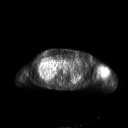
FDG PET of an extremity soft-tissue mass (from a PET/CT study), one axial slice. Slice 140 of 267 in the series (ordered by position). 3.27 mm slice thickness. 128 × 128 image matrix. Female patient, age 83 years. From the clinical record (not read from this slice): histological type: pleiomorphic leiomyosarcoma; grade: high; site of the primary tumour: left biceps.
Outlined on this slice (expert contour drawn on MRI and transferred to this co-registered scan by the dataset authors):
- gross tumour volume including surrounding oedema: box from (x=102, y=69) to (x=108, y=76) px
- gross tumour volume (mass): (x=102, y=70)–(x=106, y=72)